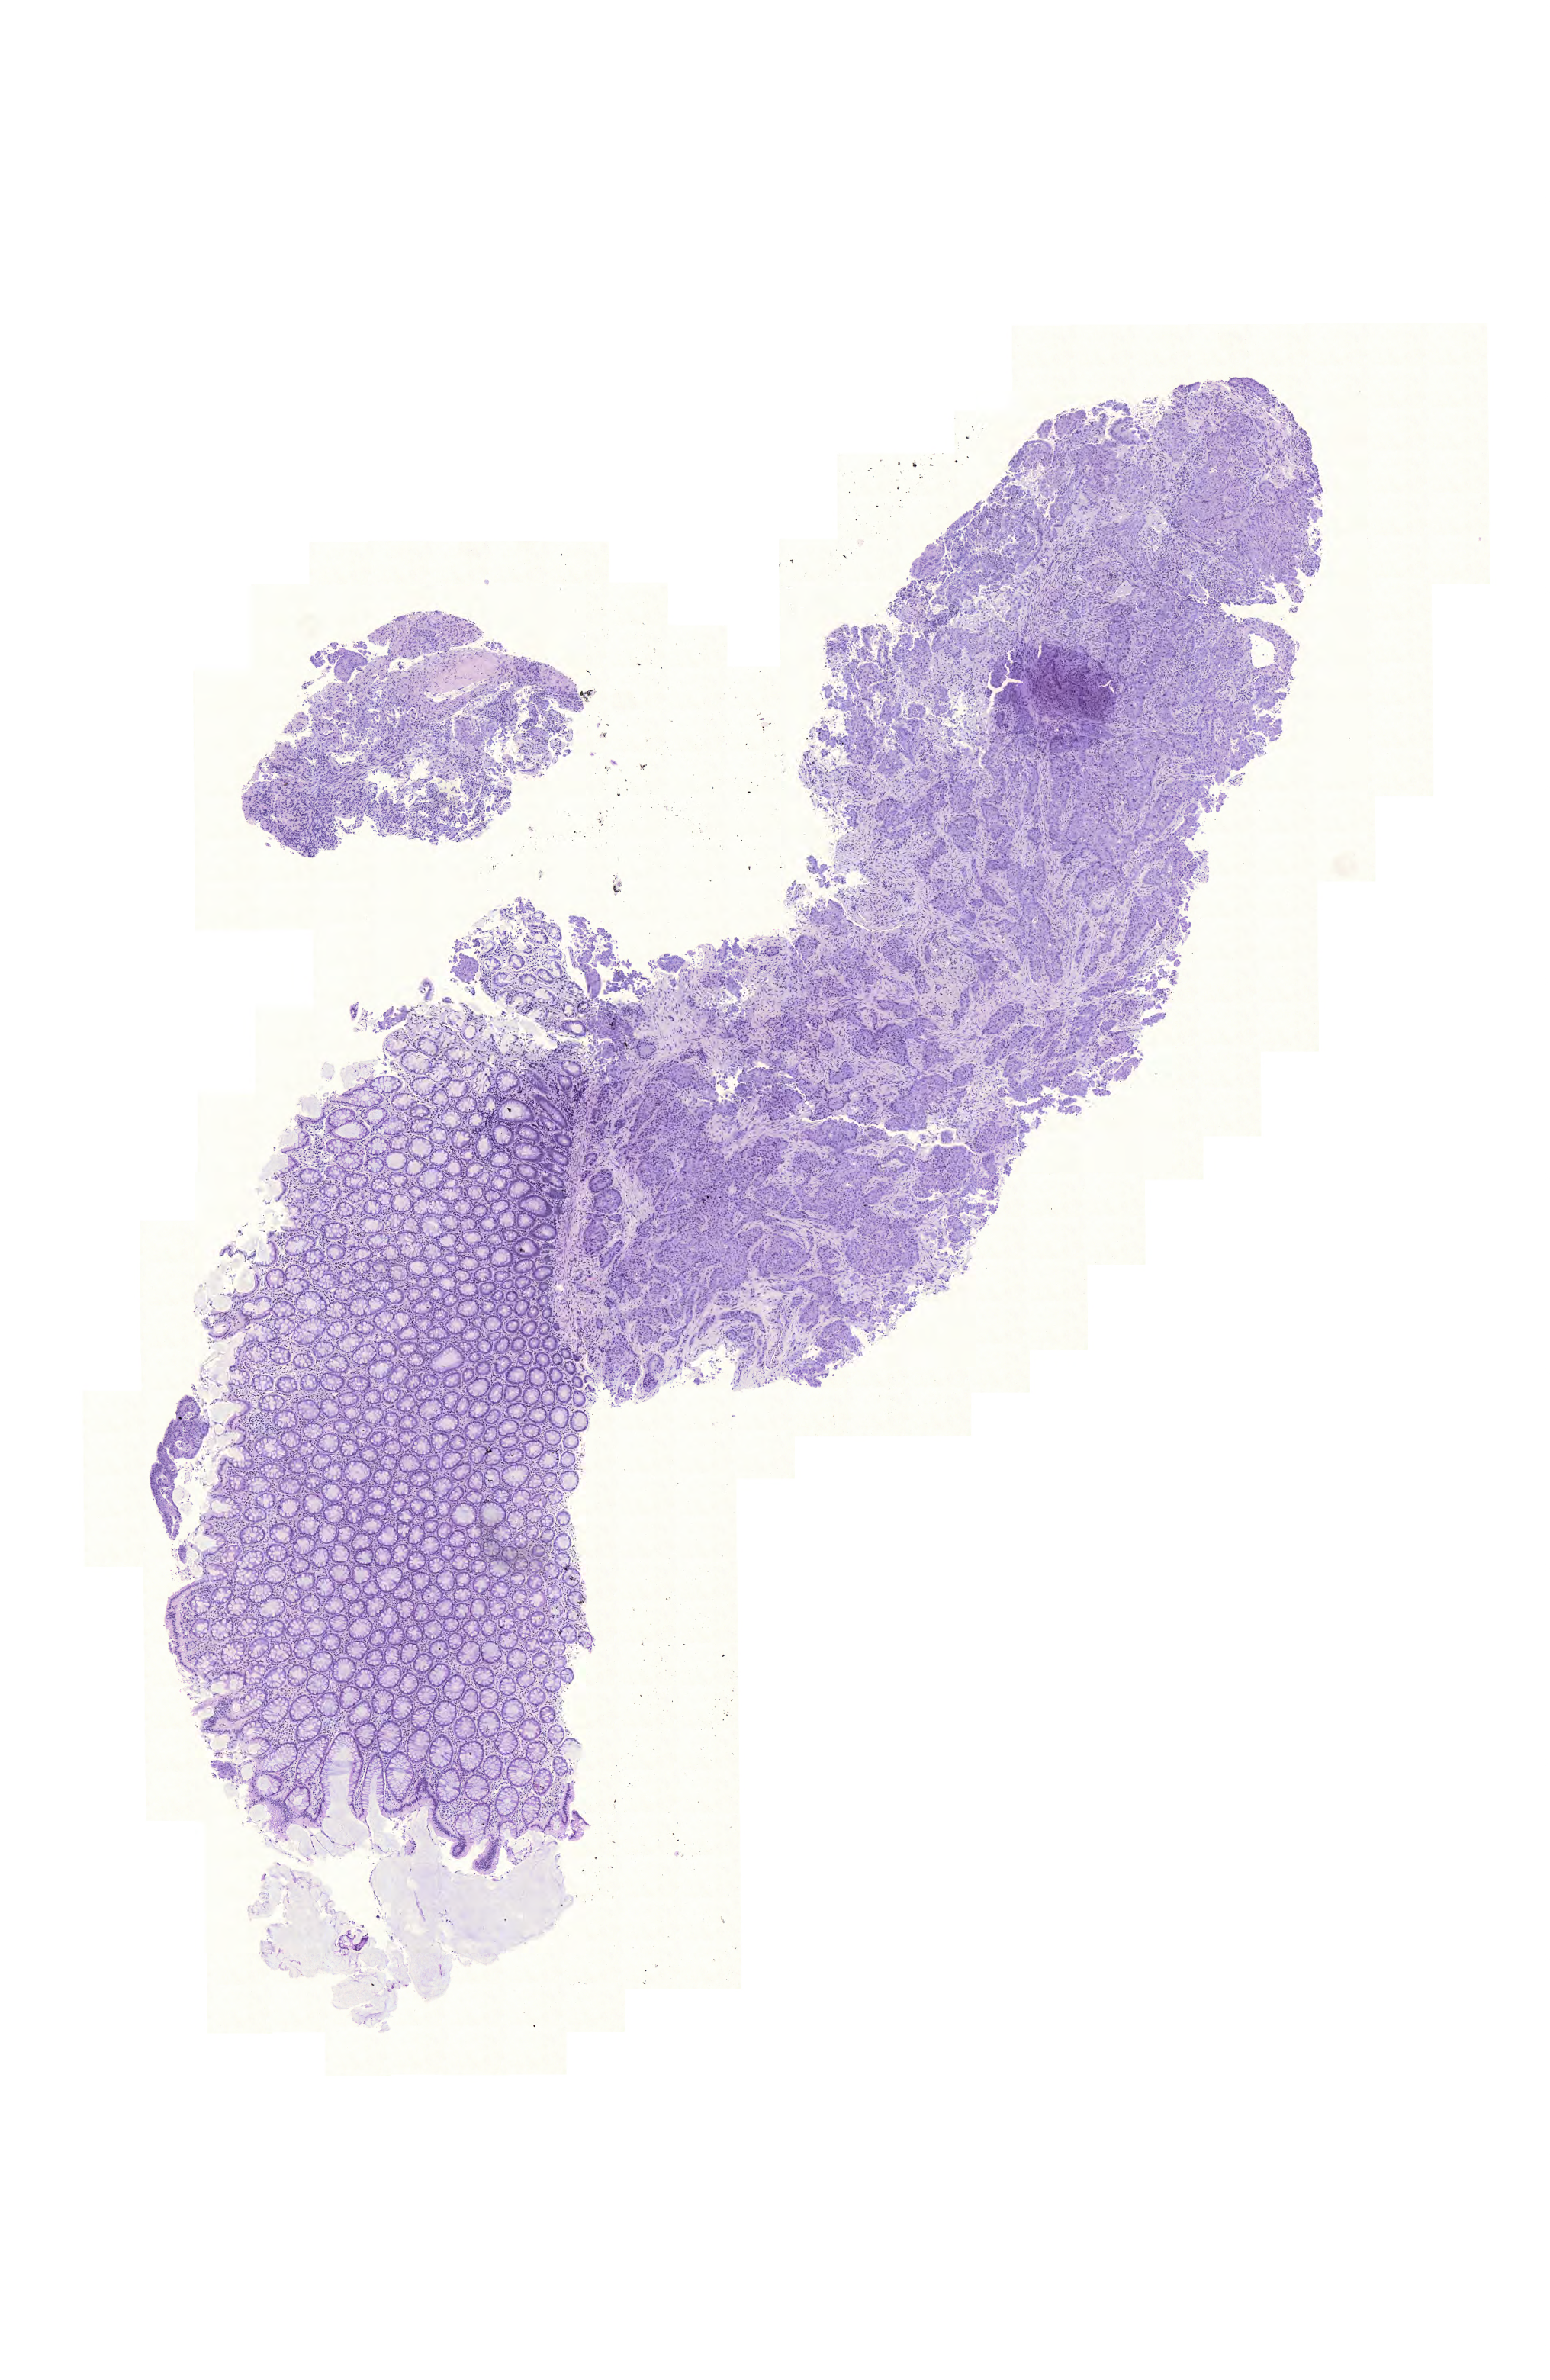
Digitized H&E tissue section (whole slide), low-resolution overview of the scanned area, about 7.6 x 11.6 mm (from a 20x scan), formalin-fixed paraffin-embedded (FFPE) diagnostic section, colon, primary tumour sample. Patient: male, age at initial diagnosis 68 years.
• lymph nodes positive (case pathology): 6 of 14 examined
• AJCC pathologic stage: IIIC (6th edition)
• diagnosis: Adenocarcinoma, NOS (descending colon)